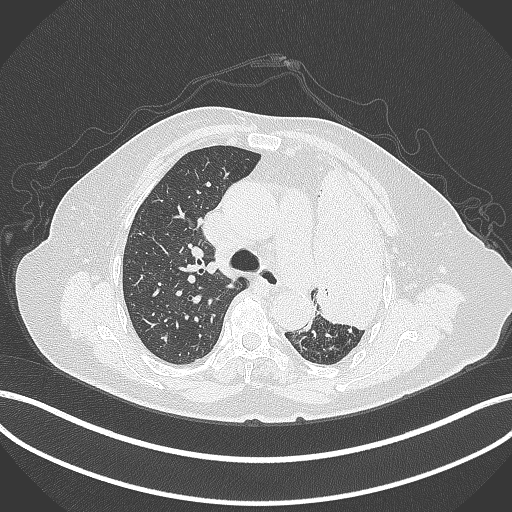
Chest CT, one axial slice; position 264 of 399 along the scan axis; 120 kVp; lung window (W 1500 / L -600 HU); 512 × 512 image matrix, field of view 400 × 400 mm. Female patient, age 75 years. From the clinical record (not read from this slice): clinical TNM (as recorded): T3 N3 M1.
Outlined on this slice (bounding box drawn by a radiologist):
- lung tumour (recorded histology: adenocarcinoma): box from (x=314, y=158) to (x=396, y=336) px